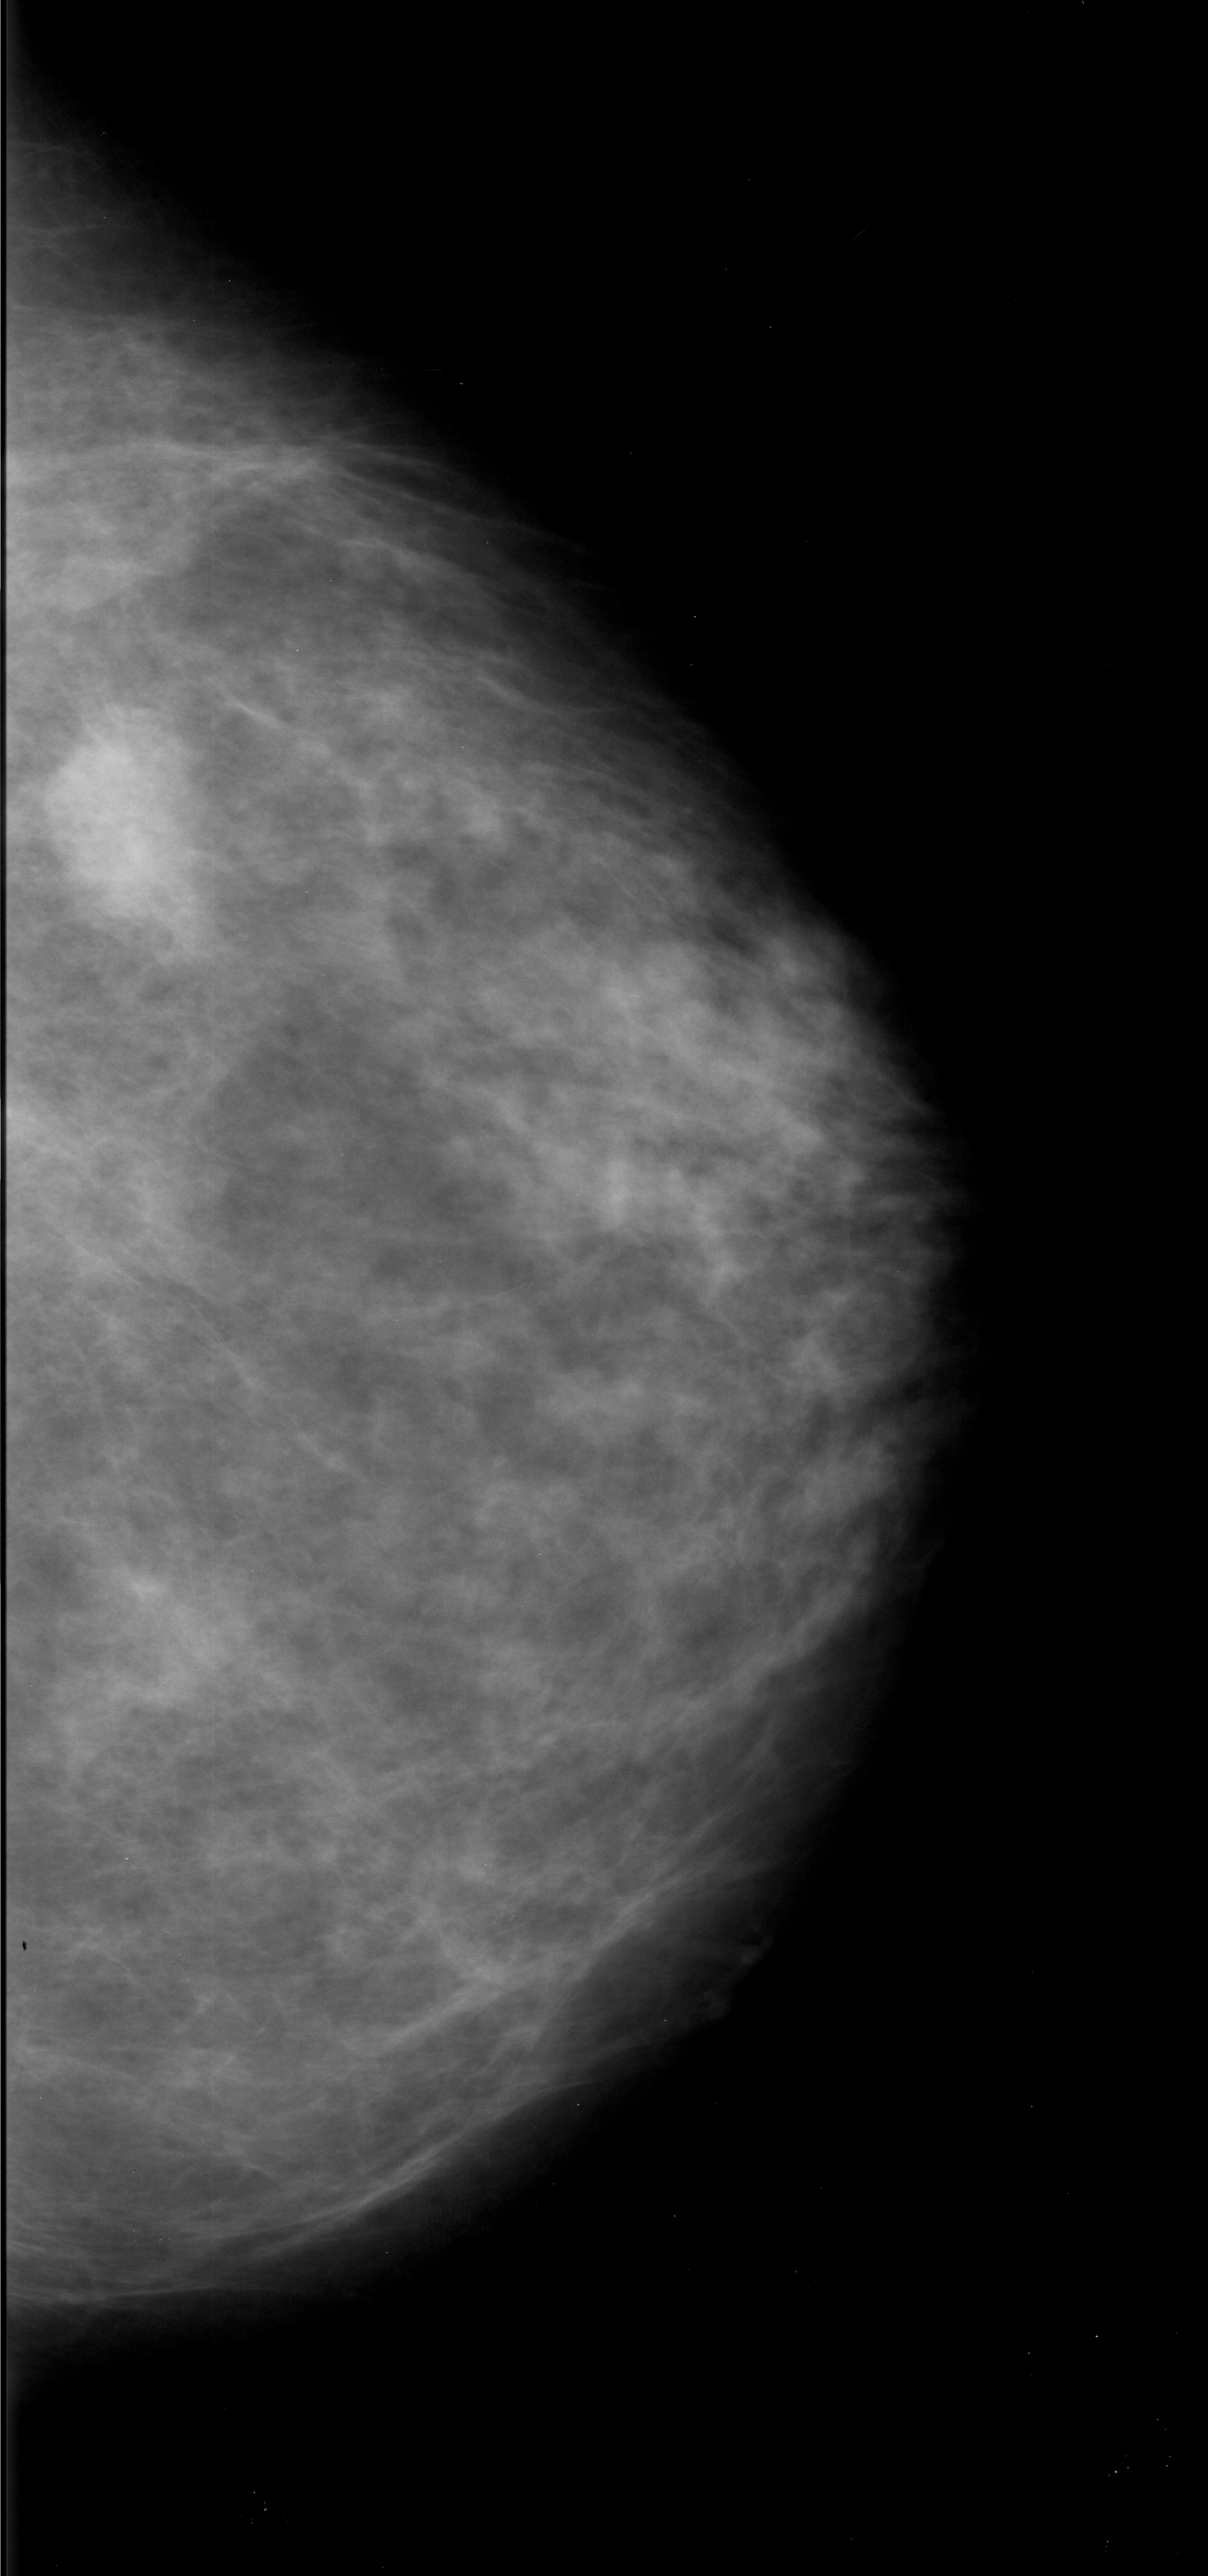
Scanned film-screen mammogram; right breast; CC view; breast composition: heterogeneously dense (BI-RADS density category 3 of 4).
Finding: mass, shape irregular, margins ill defined; BI-RADS assessment category 4; subtlety rating 4 on a 1 (subtle) to 5 (obvious) scale; pathology (as recorded): malignant.